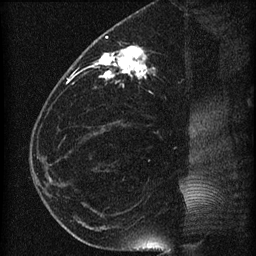
Breast MRI (dynamic contrast-enhanced), one sagittal slice; slice 27 of 60 in the series (ordered by position); dynamic contrast-enhanced series, image 2 of 4 at this slice position (ordered by acquisition); 1.5 T; TE 4.2 ms, TR 22.7 ms; 1.5 mm slice thickness; 256 × 256 image matrix, field of view 180 × 180 mm. Female patient, age 35 years. From the clinical record (not read from this slice): setting: breast cancer imaged before/during neoadjuvant chemotherapy; receptor status: HR-positive, HER2-negative.
Annotated regions visible in this slice (semi-automatically segmented with operator editing):
- analysis volume of interest (the breast-tissue region the enhancement analysis was run in; not a lesion): box from (x=69, y=27) to (x=199, y=112) px
- tumour enhancement mask (voxels above the 90 % enhancement threshold inside the analysis volume of interest): (x=69, y=45)–(x=148, y=81)